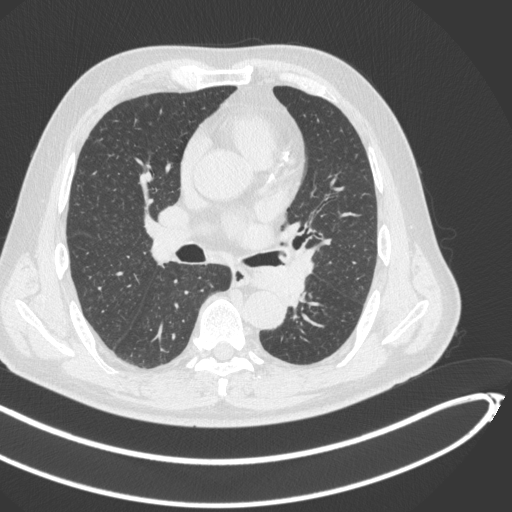
Chest CT, one axial slice; slice 258 of 466 in the series (ordered by position); 120 kVp; lung window (W 1500 / L -600 HU); 1 mm slice thickness; 512 × 512 image matrix, field of view 400 × 400 mm. Patient: male, 64 years. Case-level facts recorded for this patient, not image findings: clinical TNM (as recorded): T1c N0 M0; histopathological grade: G2.
Outlined on this slice (bounding box drawn by a radiologist):
- lung tumour (recorded histology: squamous cell carcinoma): box from (x=251, y=258) to (x=311, y=302) px